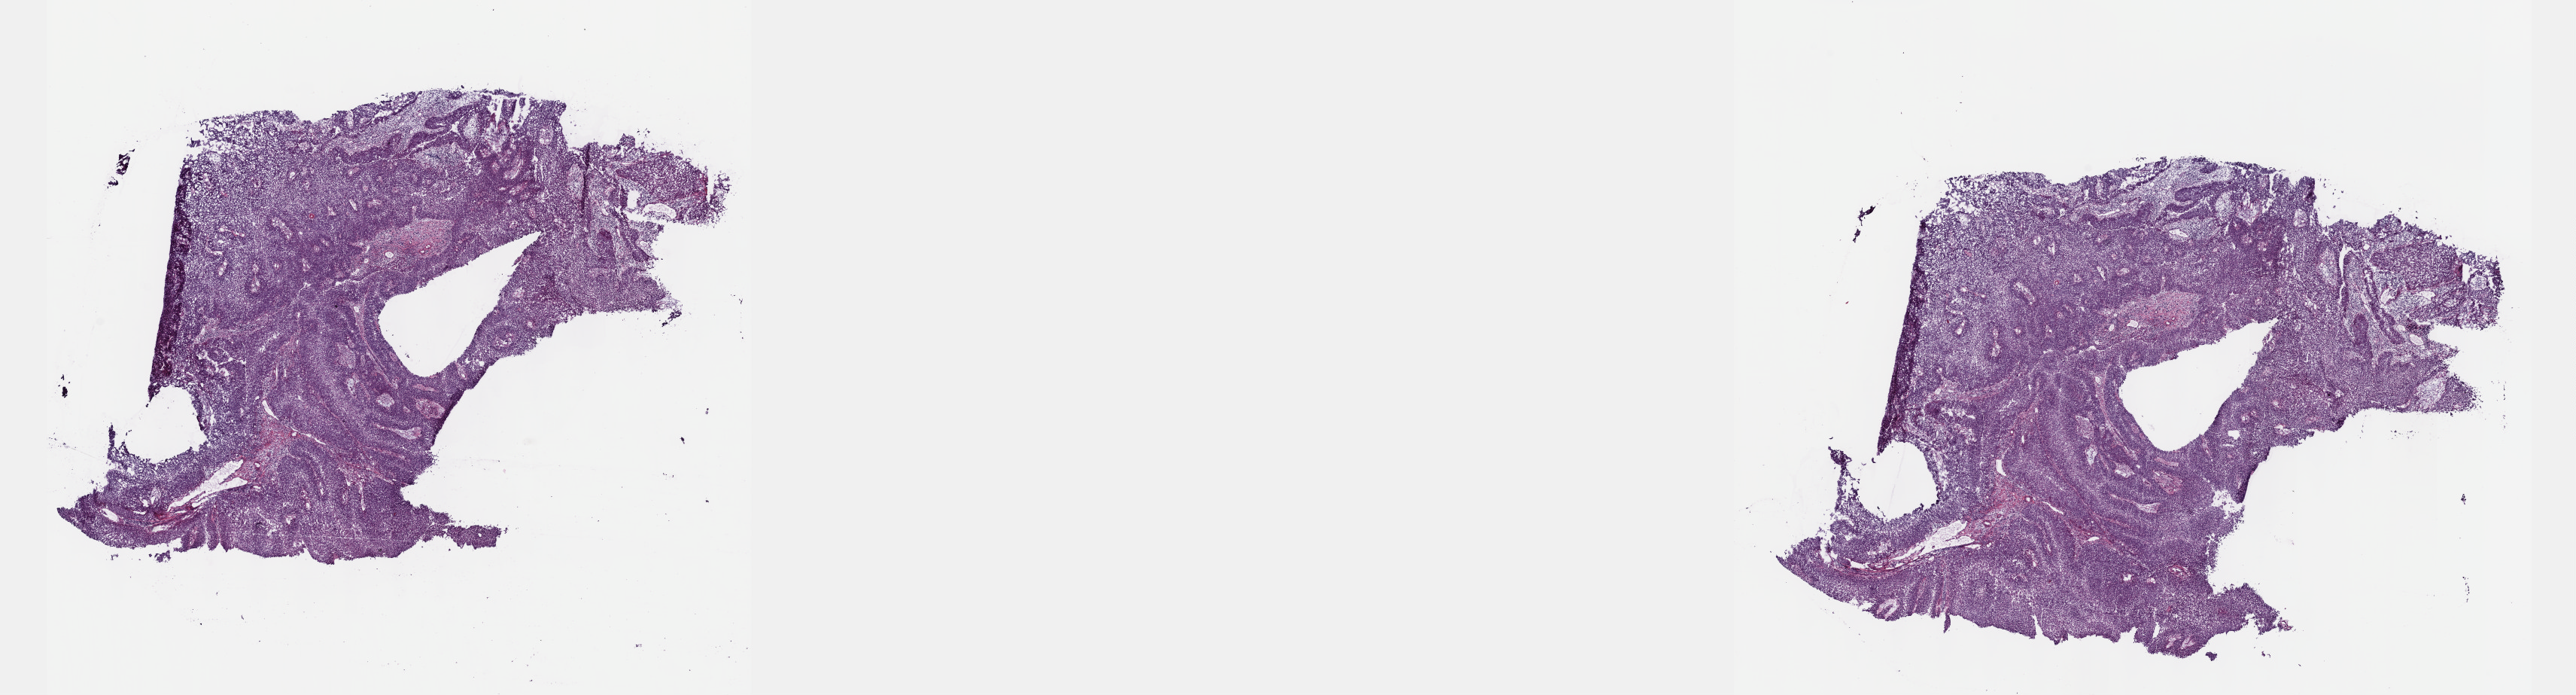
H&E-stained whole-slide image — a low-resolution overview of the entire scanned area, about 27.7 x 7.5 mm (slide scanned at 40x). Frozen section. Sample: primary tumour, bladder. Male patient; age at initial diagnosis 64 years. Composition of this section per pathologist review: tumour cells 80%, tumour nuclei 80%.
Pathologic diagnosis: Papillary transitional cell carcinoma (lateral wall of bladder).